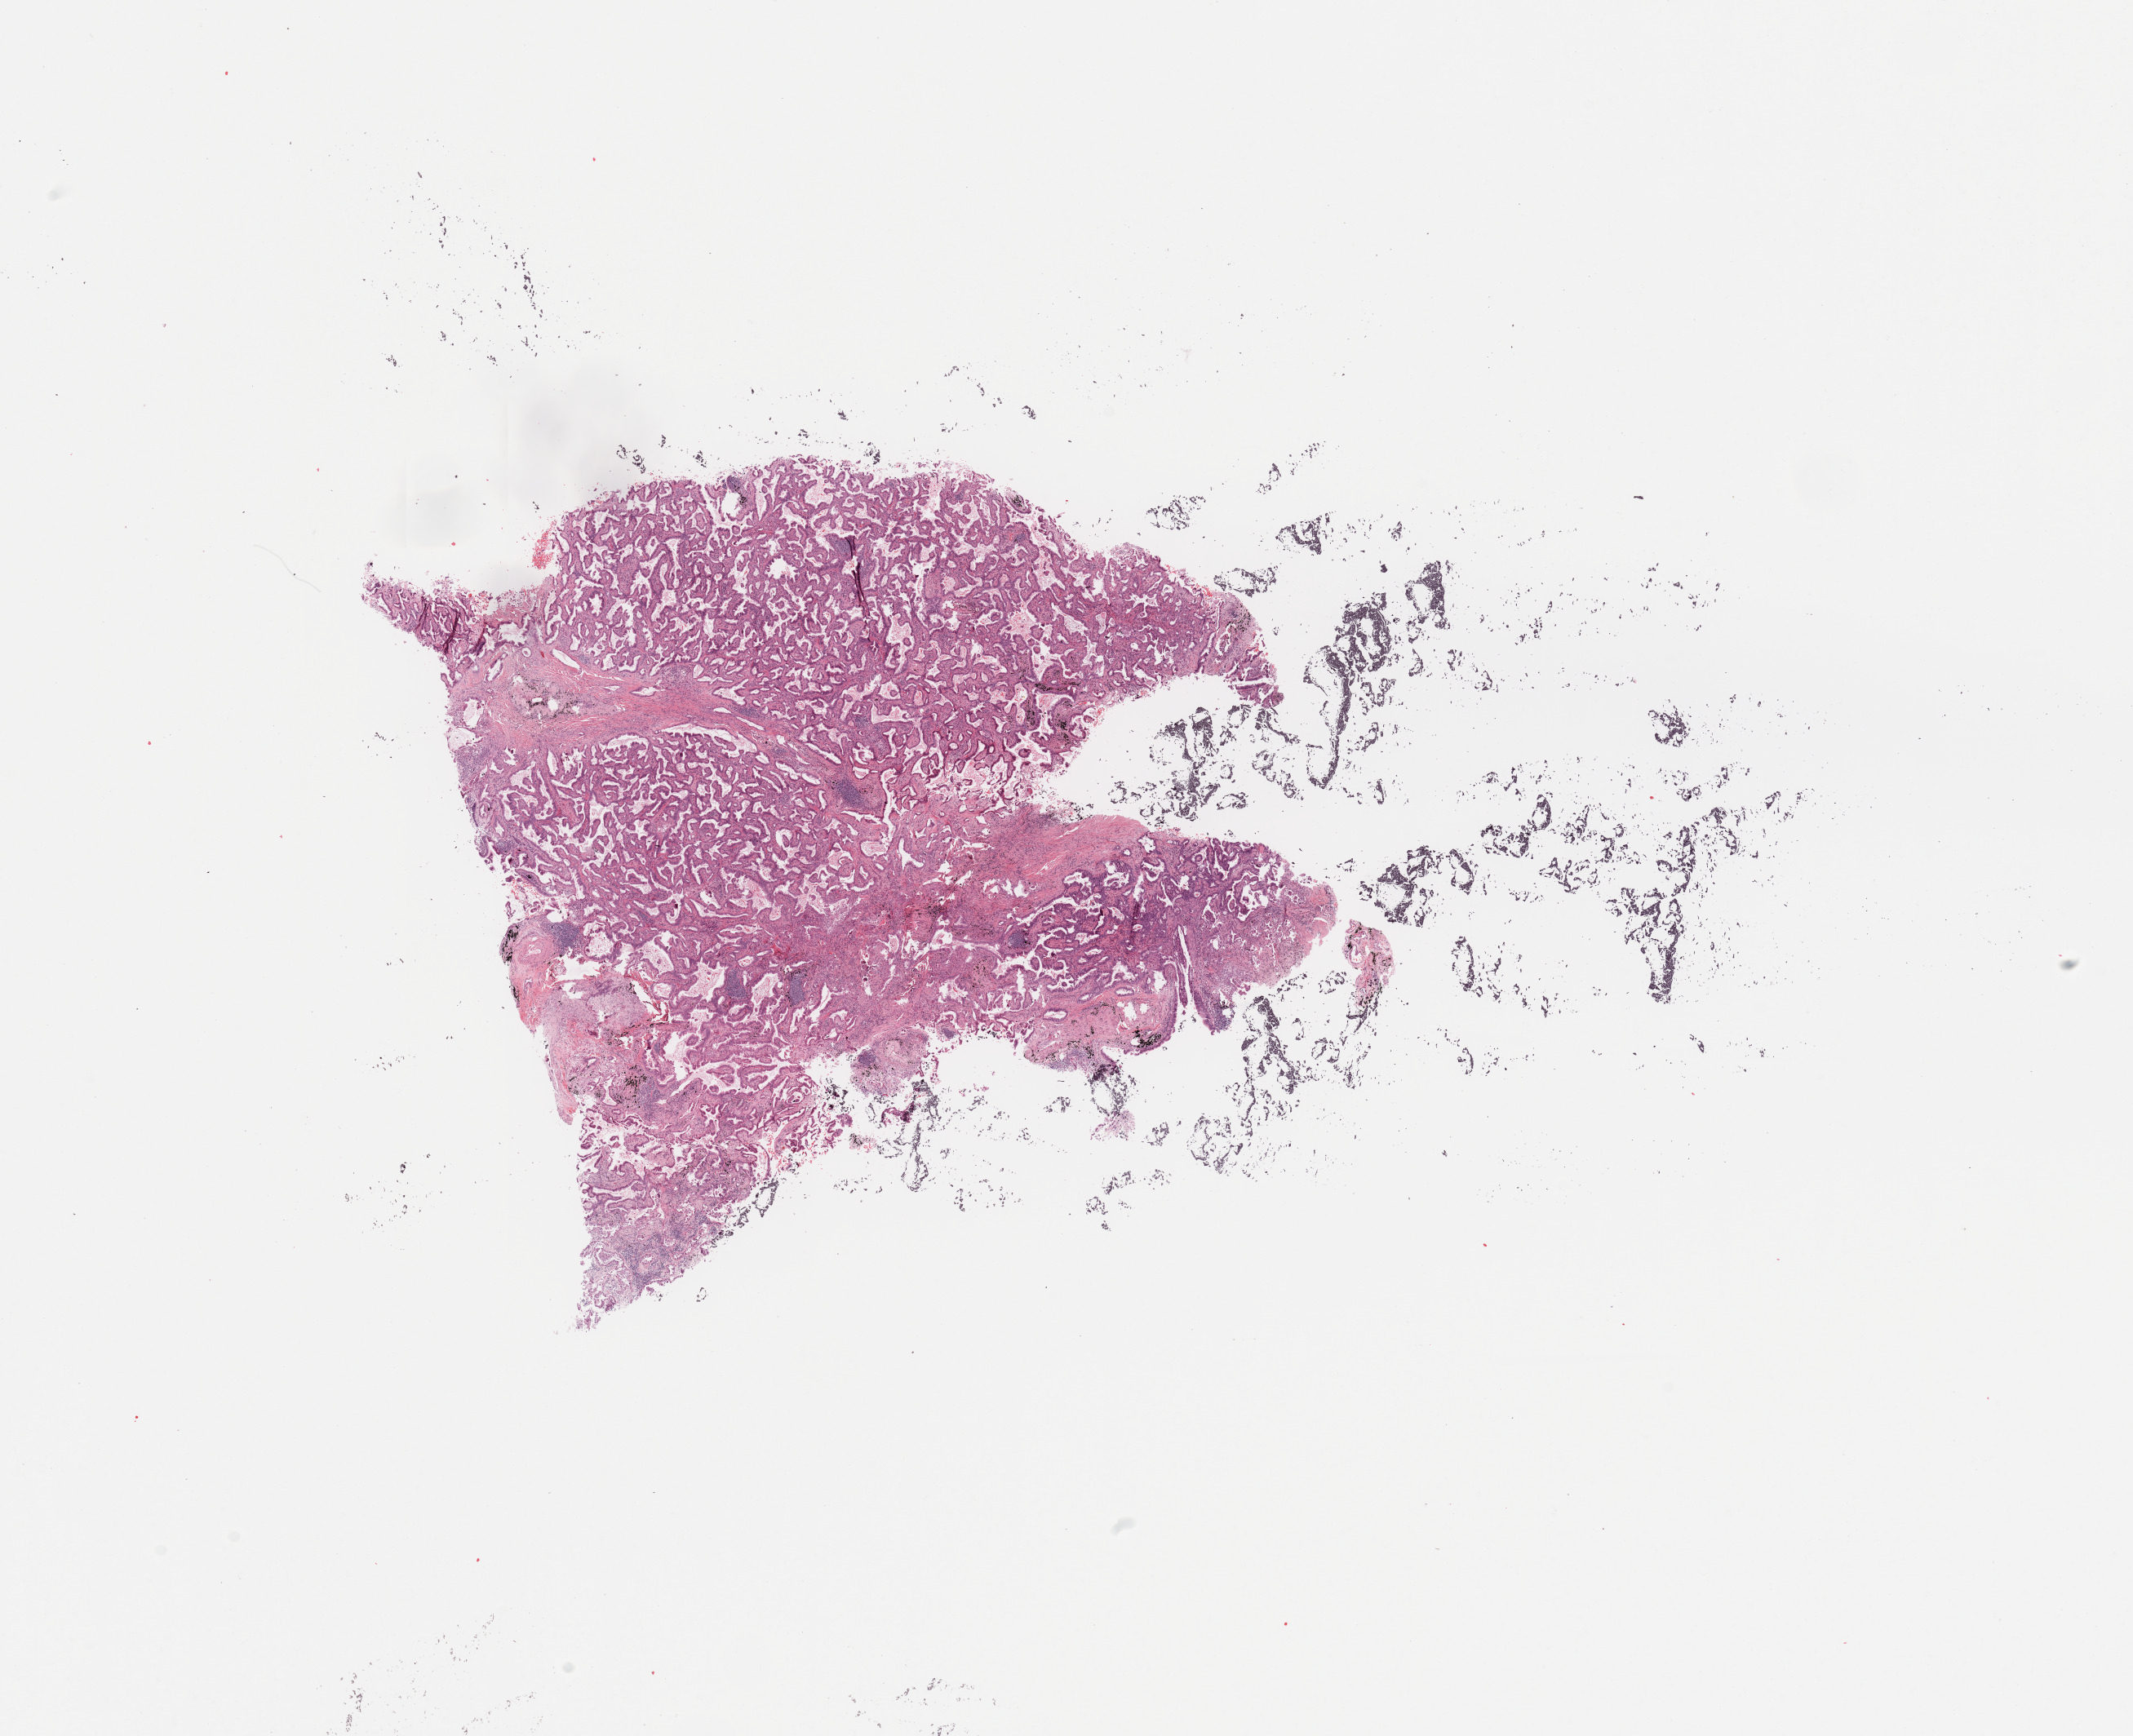
Whole-slide histology image, H&E-stained — shown as a low-resolution overview of the whole scanned area (about 20.7 x 16.8 mm). Tumour tissue sample, sampled site: lung. 68-year-old male patient. Histologic grade: G2 (moderately differentiated). Slide review estimates, as recorded: tumour nuclei 75%, necrosis 5%.
AJCC pathologic stage: IA. Primary tumour site (as recorded): right lower lobe. Diagnosis: Adenocarcinoma, NOS.